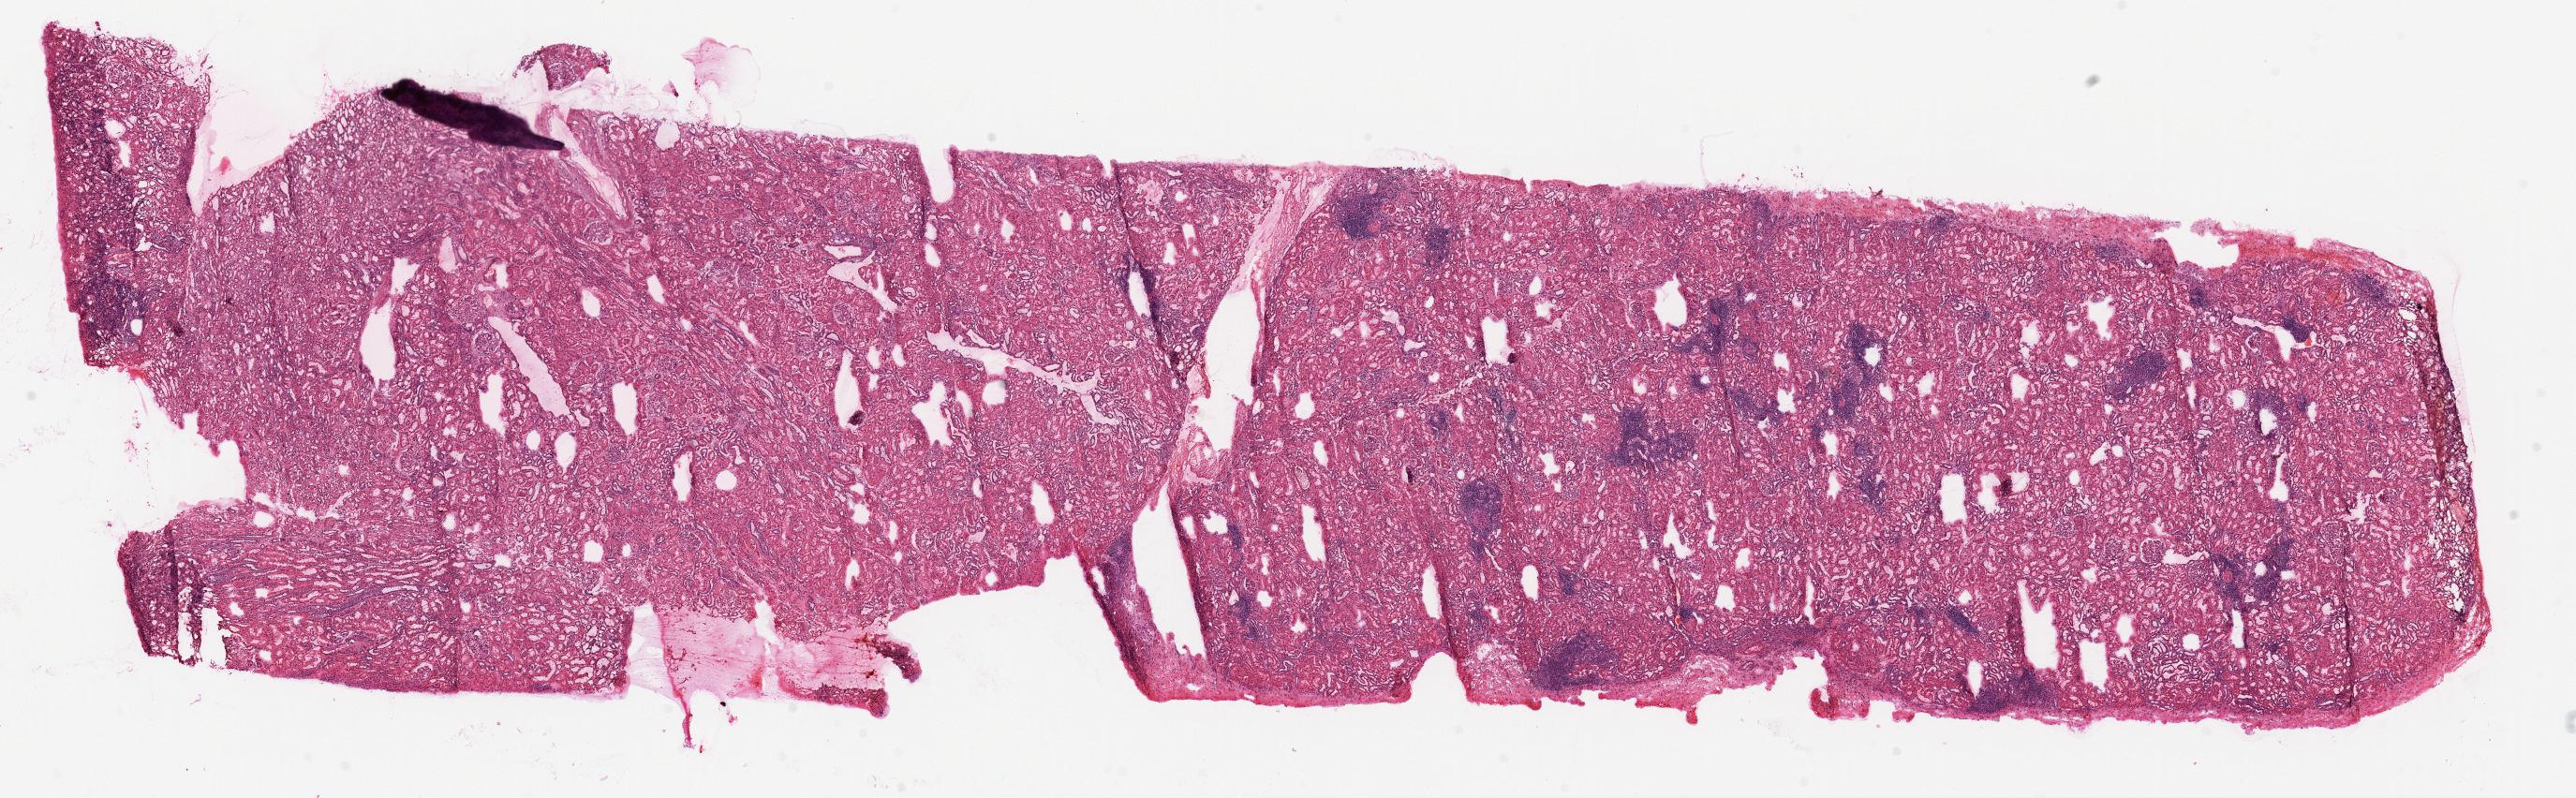
Digitized H&E-stained tissue section (whole slide), a low-resolution overview of the entire scanned area, about 22.1 x 6.8 mm. Frozen section. Sample: solid tissue normal (non-tumour tissue), kidney. Female patient; age at initial diagnosis 67 years.
This section: solid tissue normal (non-tumour) sample from the same patient. Patient diagnosis: Clear cell adenocarcinoma, NOS.